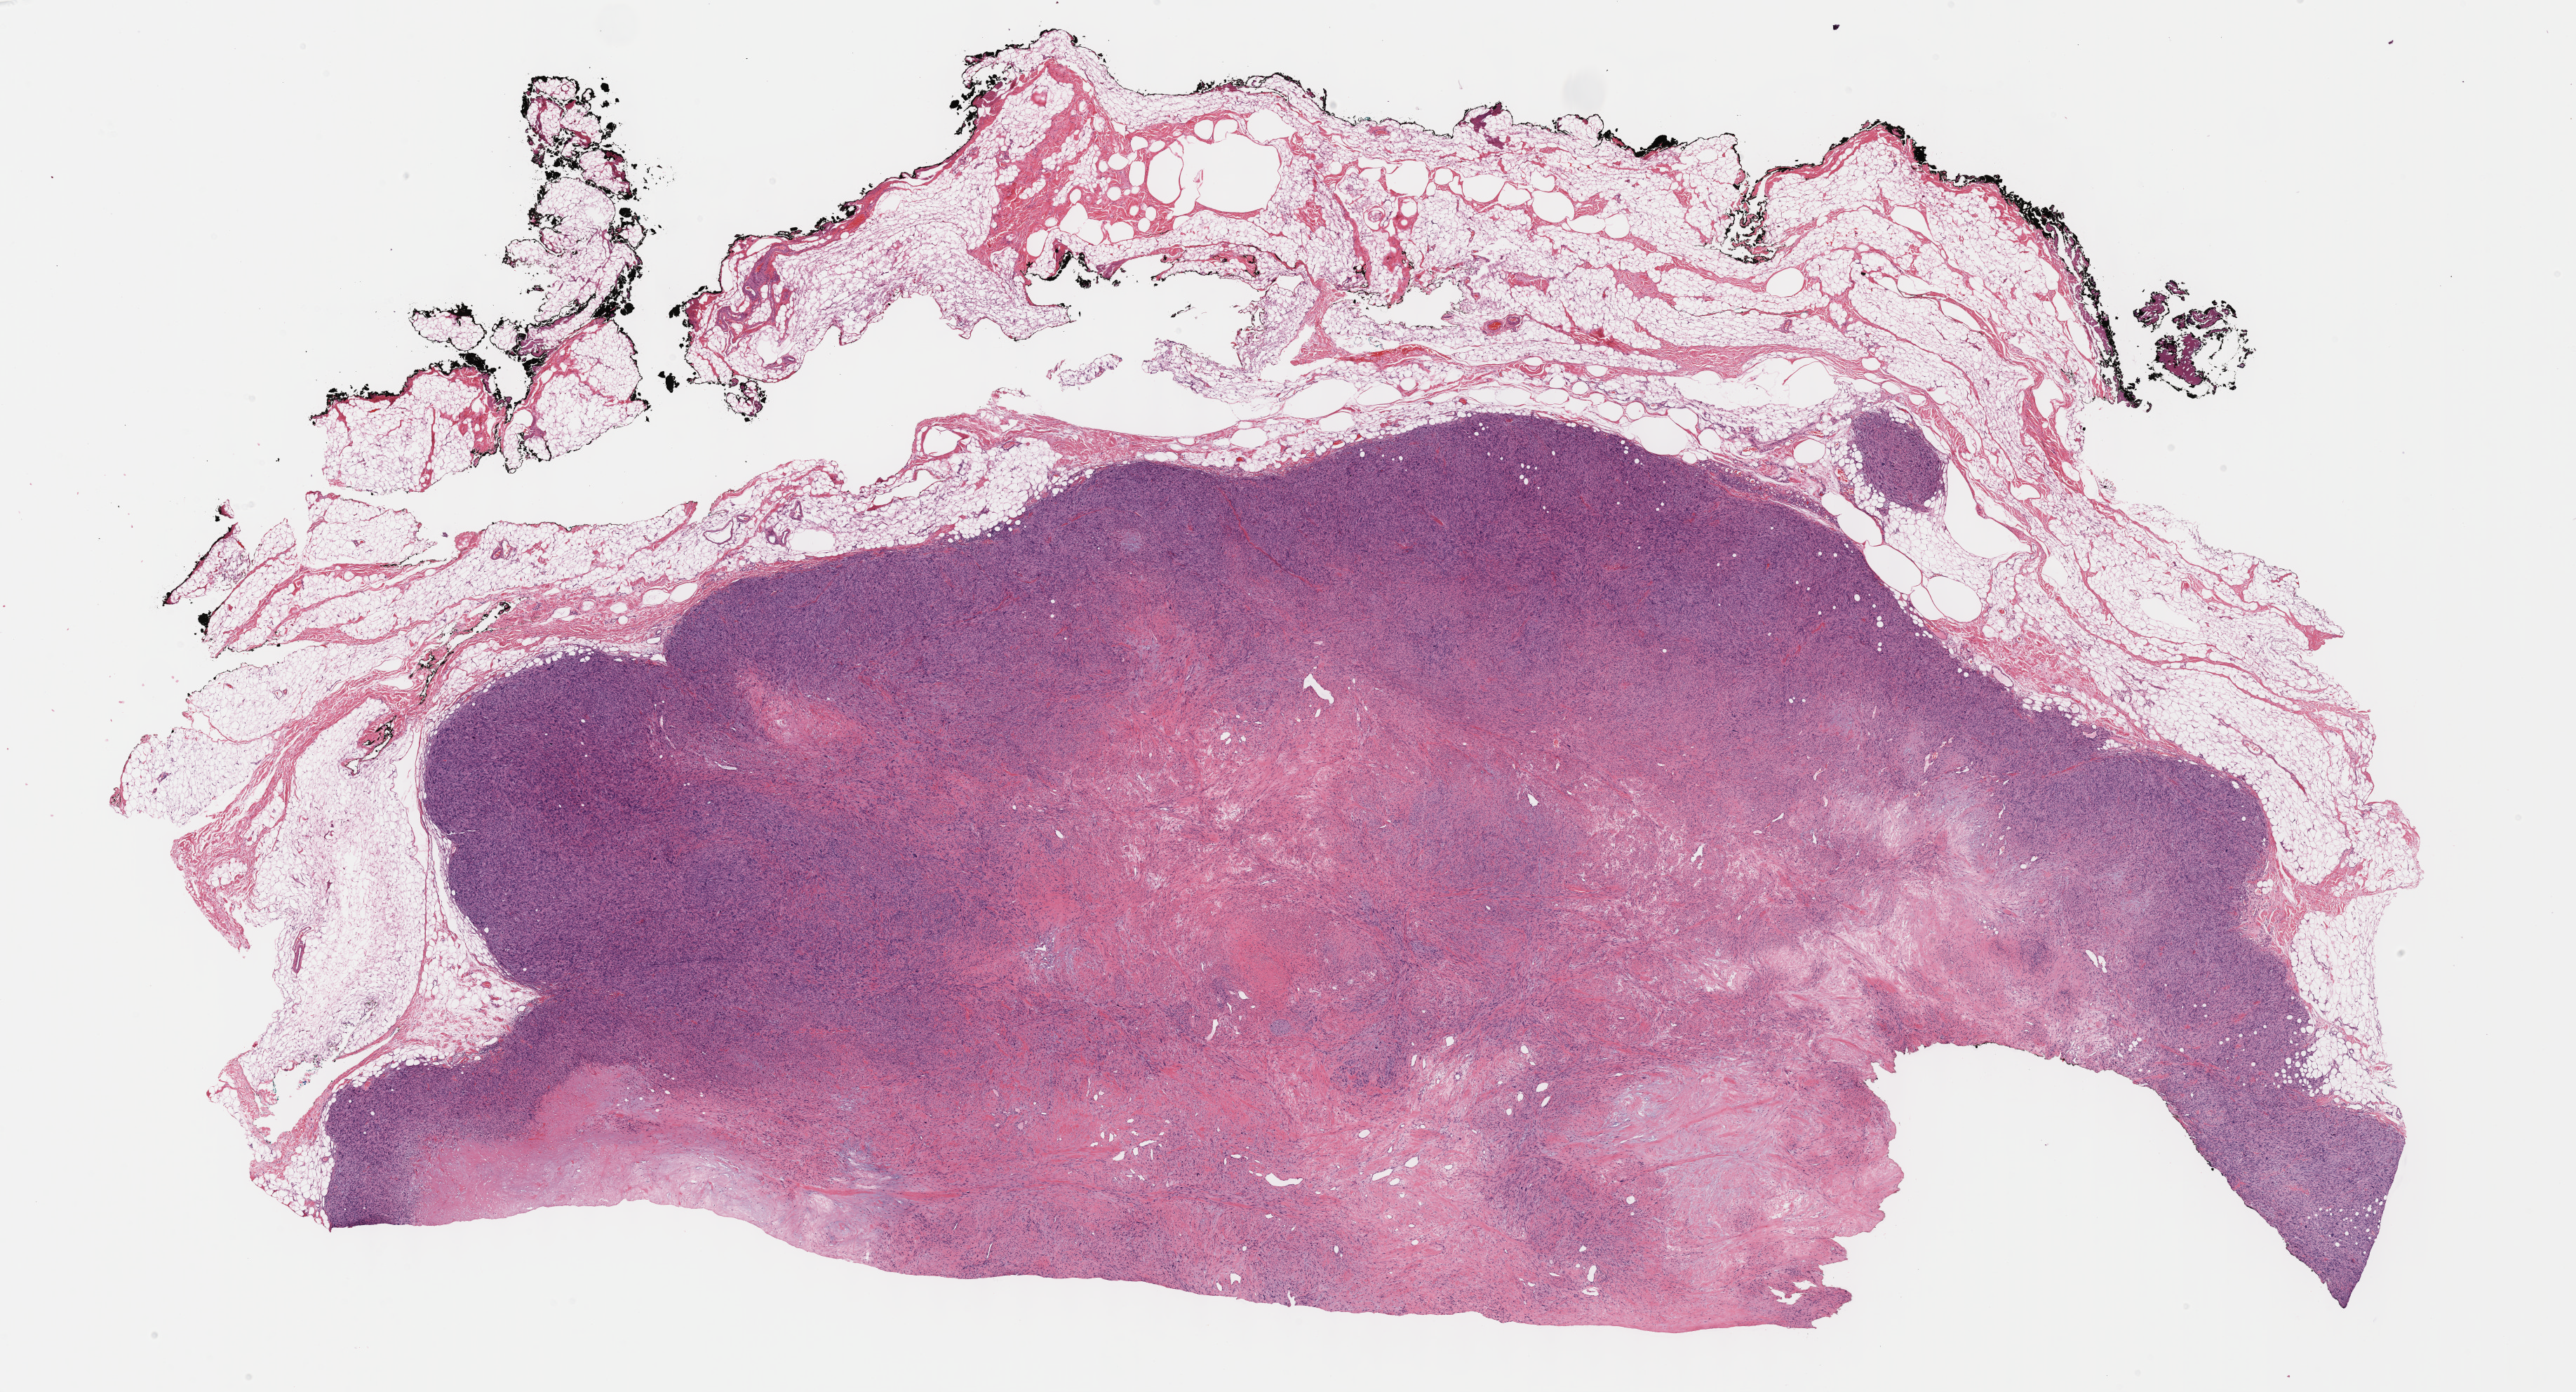
Whole-slide histology image, Hematoxylin and eosin (H&E) stained, low-resolution overview of the scanned area, about 29.7 x 16.0 mm (from a 40x scan), formalin-fixed paraffin-embedded (FFPE) diagnostic section, connective, subcutaneous and other soft tissues, primary tumour sample. Female, age 52 years at initial diagnosis.
• diagnosis: Leiomyosarcoma, NOS